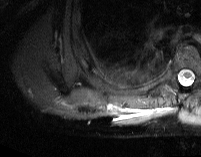
MRI of an extremity soft-tissue mass, one axial slice. Position 13 of 74 along the scan axis. STIR. MR volume resampled by the dataset authors to the PET/CT grid (not the native acquisition matrix). 3.27 mm slice thickness. 201 × 157 image matrix, field of view 196 × 153 mm. Male patient. From the clinical record (not read from this slice): histological type: pleiomorphic spindle cell undifferentiated; grade: high; site of the primary tumour: right parascapusular.
Structures marked on this image (expert contour drawn on MRI and transferred to this co-registered scan by the dataset authors):
- gross tumour volume including surrounding oedema: bounding box [x1, y1, x2, y2] px = [106, 103, 171, 124]